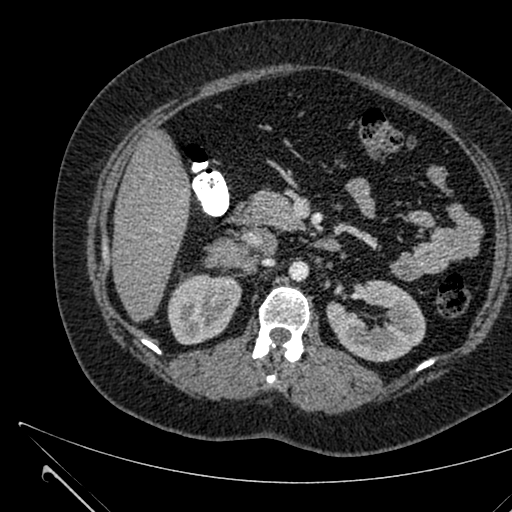
Contrast-enhanced abdominal CT, one axial slice. Position 354 of 731 along the scan axis. Intravenous contrast given. Soft-tissue window (W 400 / L 40 HU). 1 mm slice thickness. 512 × 512 image matrix, field of view 376 × 376 mm. Female patient, age 36 years. From the clinical record (not read from this slice): diagnosis: adrenocortical carcinoma; tumour side: right adrenal; tumour size at pathology: 10 cm; Ki-67 index: 20 %.
Structures marked on this image (semi-automatic segmentation, software-assisted and operator-edited):
- mass: bounding box (x1, y1, x2, y2) in pixels: (208, 238, 249, 268)